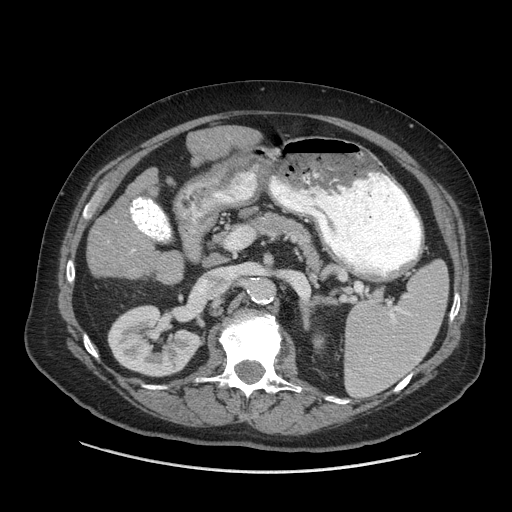
Contrast-enhanced abdominal CT (liver protocol), one axial slice. Slice 26 of 77 in the series (ordered by position). Reconstruction kernel STANDARD. 140 kVp. Soft-tissue window (W 400 / L 40 HU). 512 × 512 image matrix, field of view 420 × 420 mm. From the clinical record (not read from this slice): diagnosis: hepatocellular carcinoma (patient treated with transarterial chemoembolisation; whether this scan precedes or follows treatment is not stated here); TNM stage (as recorded): Stage-I; Child-Pugh class: A.
Annotated regions visible in this slice (semi-automatic segmentation, software-assisted and operator-edited):
- liver parenchyma outside the tumour (the mass and vessels are separate outlines, so this box may not span the whole liver): bounding box <90,132,206,282> (left, top, right, bottom; pixels)
- liver vessels: <132,249,135,252>